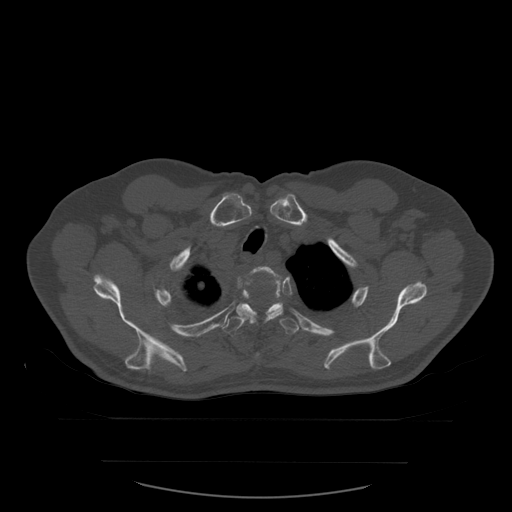
CT including the spine, one axial slice. Position 454 of 590 along the scan axis. Bone window (W 1800 / L 400 HU). 1.25 mm slice thickness. 512 × 512 image matrix. Patient age 71 years. From the clinical record (not read from this slice): primary cancer: lung.
Outlined on this slice (semi-automatically segmented with operator editing):
- T2 vertebra: bounding box (x1, y1, x2, y2) in pixels: (252, 267, 282, 280)
- T3 vertebra: (236, 277, 284, 321)
- T4 vertebra: (222, 295, 300, 337)